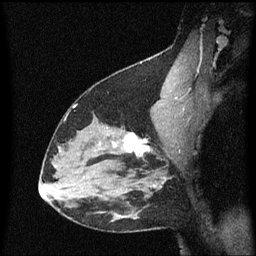
Breast MRI (dynamic contrast-enhanced), one sagittal slice; slice 40 of 60 in the series (ordered by position); dynamic contrast-enhanced series, image 2 of 3 at this slice position (ordered by acquisition); 1.5 T; TE 4.2 ms, TR 8.4 ms; 2 mm slice thickness; 256 × 256 image matrix, field of view 200 × 200 mm. Patient: female, 38 years. Case-level facts recorded for this patient, not image findings: setting: breast cancer imaged before/during neoadjuvant chemotherapy; receptor status: HR-positive, HER2-negative.
Outlined on this slice (semi-automatic segmentation, software-assisted and operator-edited):
- analysis volume of interest (the breast-tissue region the enhancement analysis was run in; not a lesion): bounding box <122,126,154,161> (left, top, right, bottom; pixels)
- tumour enhancement mask (voxels above the 70 % enhancement threshold inside the analysis volume of interest): <125,134,152,157>